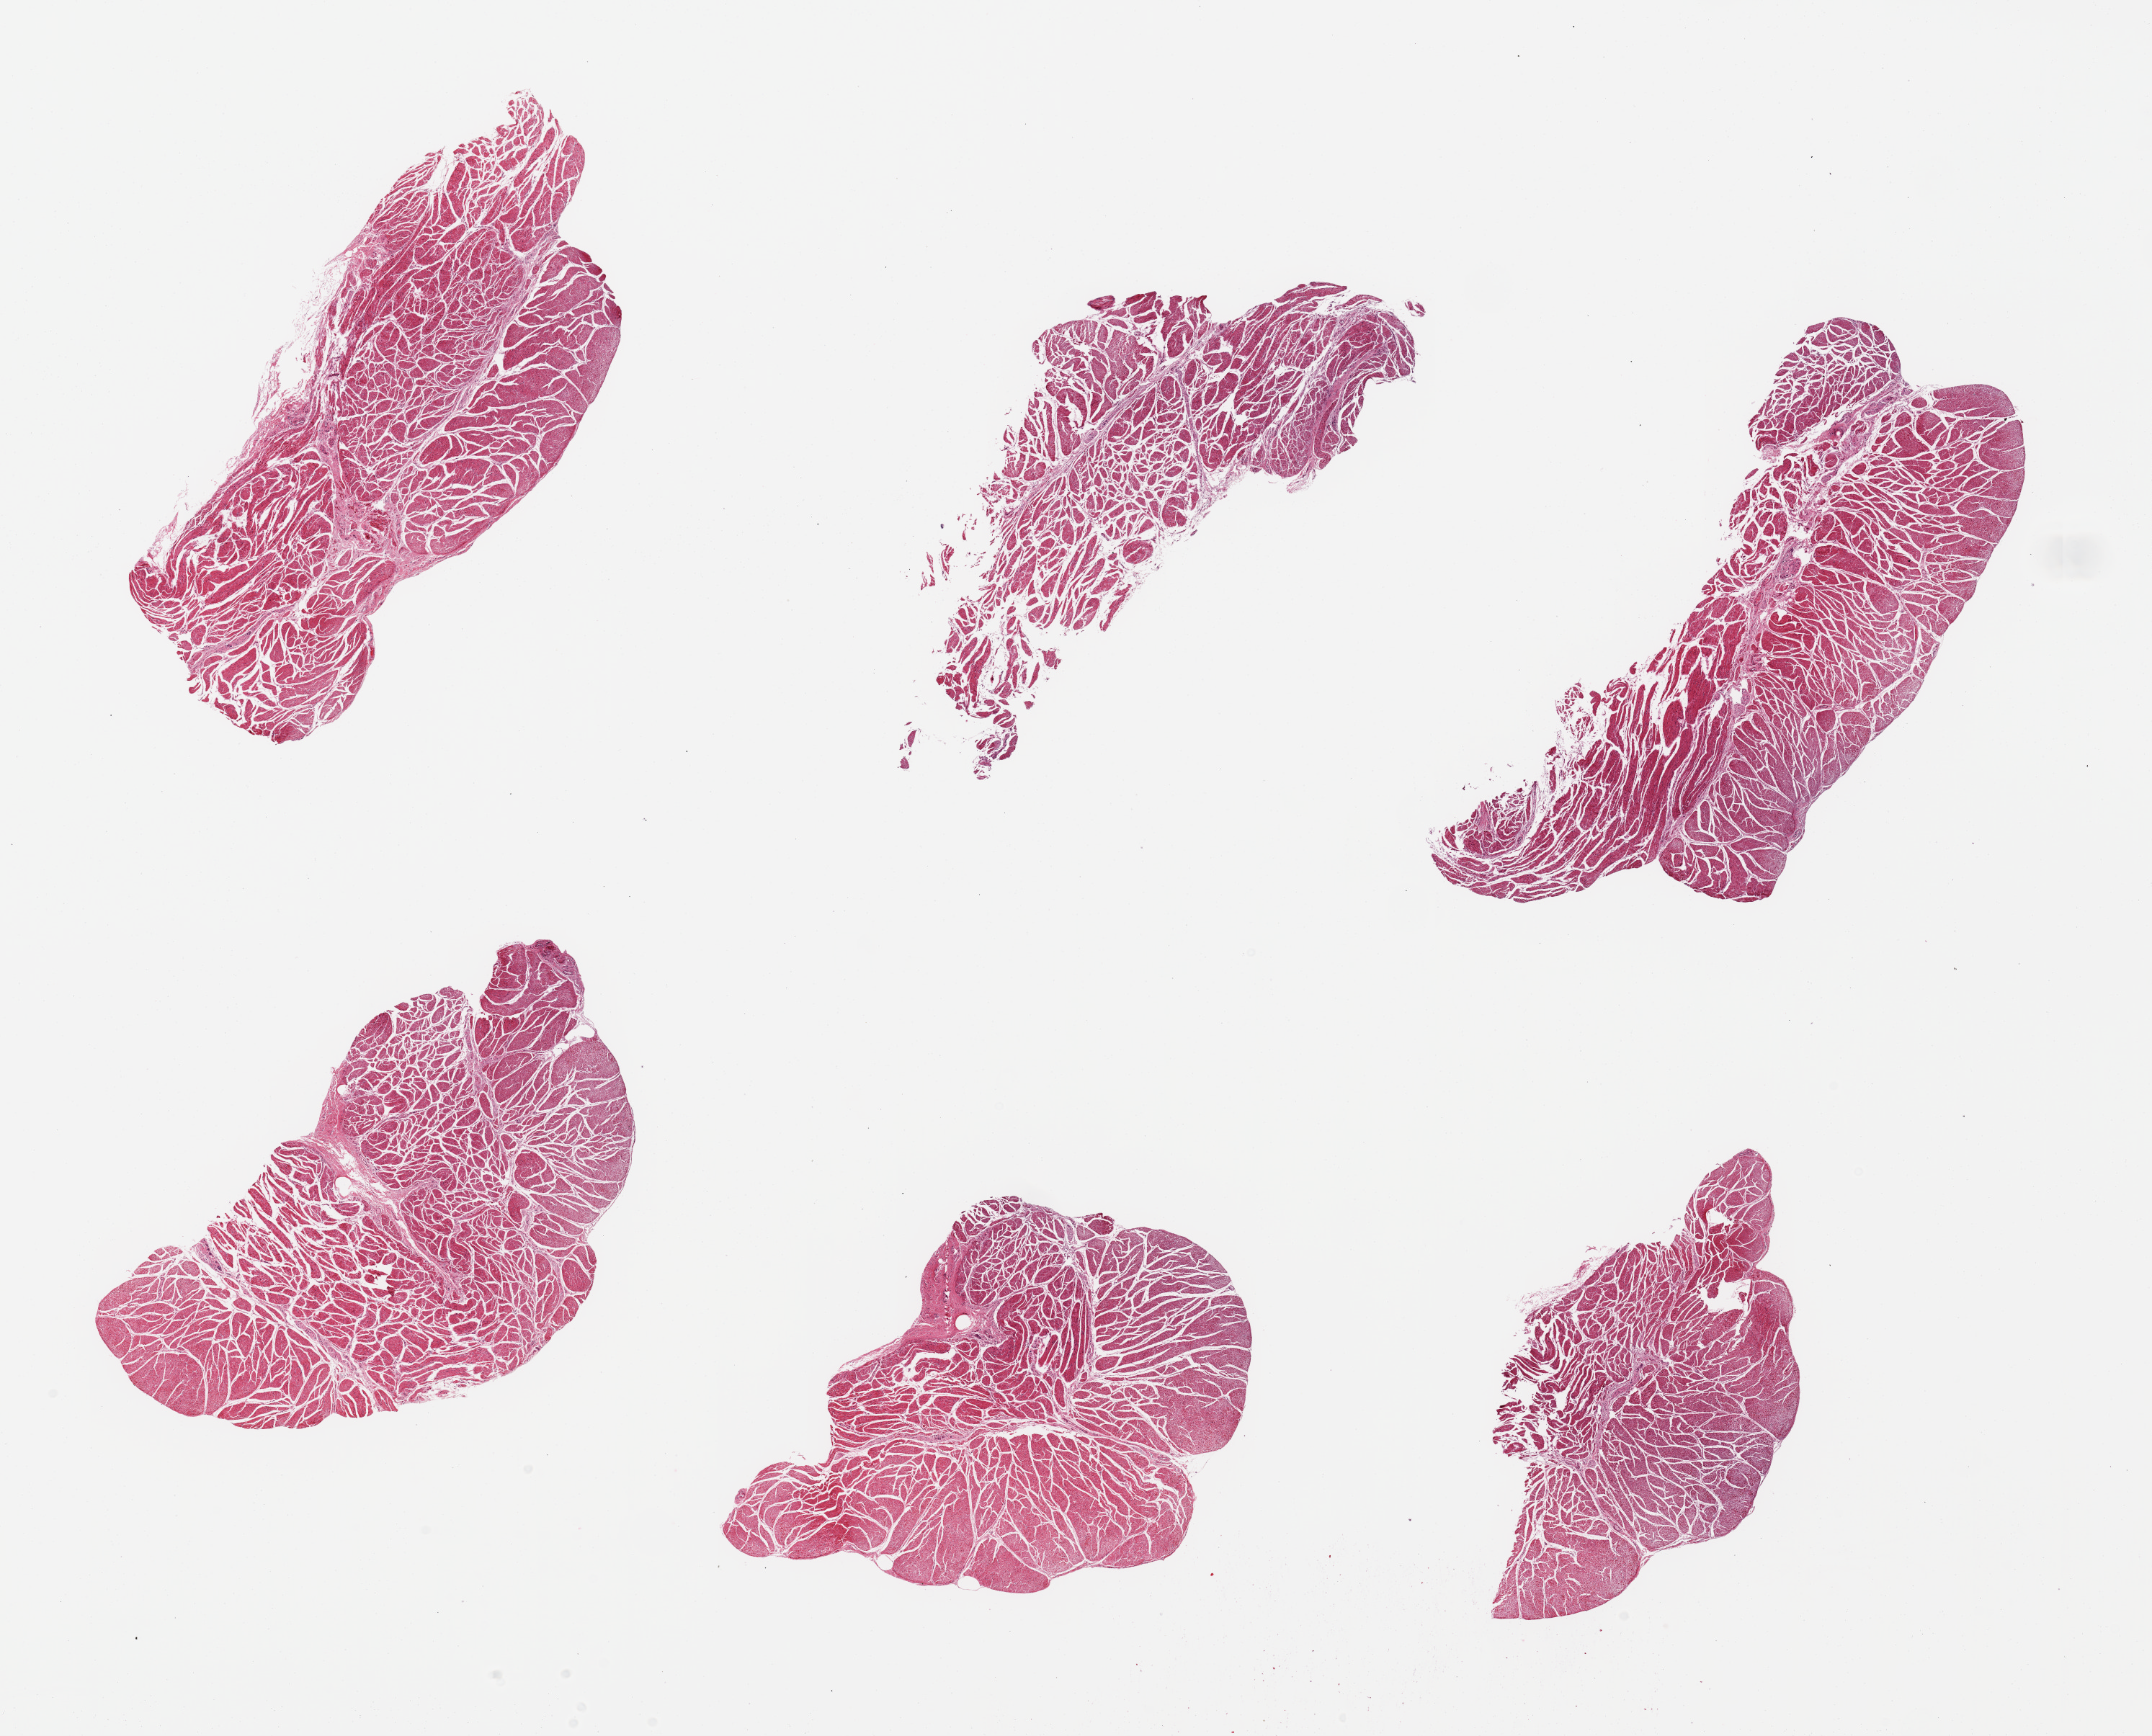
Whole-slide image, haematoxylin and eosin stain, brightfield — a low-resolution overview of the entire scanned area, about 23.6 x 19.1 mm, PAXgene-fixed paraffin-embedded (PFPE) section, target tissue: esophageal muscle, donor tissue sample. Female donor.
Review note (as recorded): 6 pieces; well trimmed.